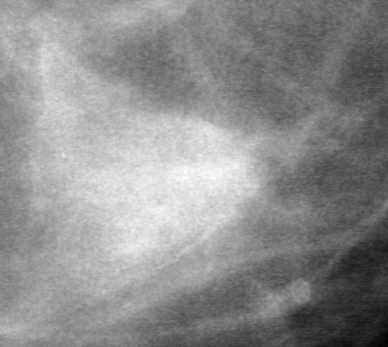
Region of interest cut from a scanned film mammogram (one marked finding), left breast, MLO view.
Marked abnormality: mass, shape irregular, margins obscured; BI-RADS assessment category 0 (incomplete: needs additional imaging); subtlety rating 5 on a 1 (subtle) to 5 (obvious) scale; pathology result (as recorded, not read from the image): benign.